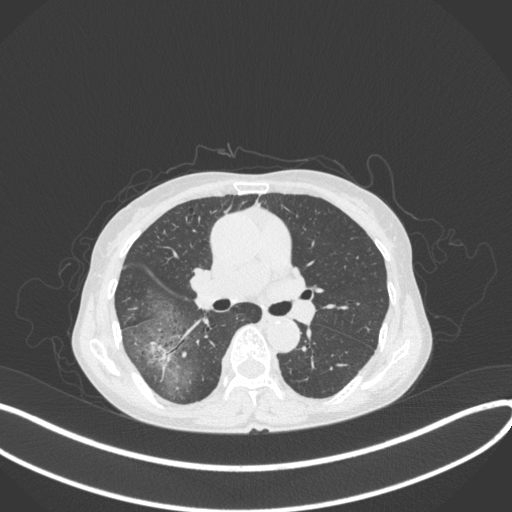
Chest CT, one axial slice; slice 230 of 379 in the series (ordered by position); reconstruction kernel B31f; lung window (W 1500 / L -600 HU); 1 mm slice thickness; 512 × 512 image matrix. Female patient, age 69 years. Case-level facts recorded for this patient, not image findings: clinical TNM (as recorded): T1b N0 M0; histopathological grade: G2-3.
Outlined on this slice (bounding box drawn by a radiologist):
- lung tumour (recorded histology: adenocarcinoma): bounding box [x1, y1, x2, y2] px = [146, 336, 176, 378]